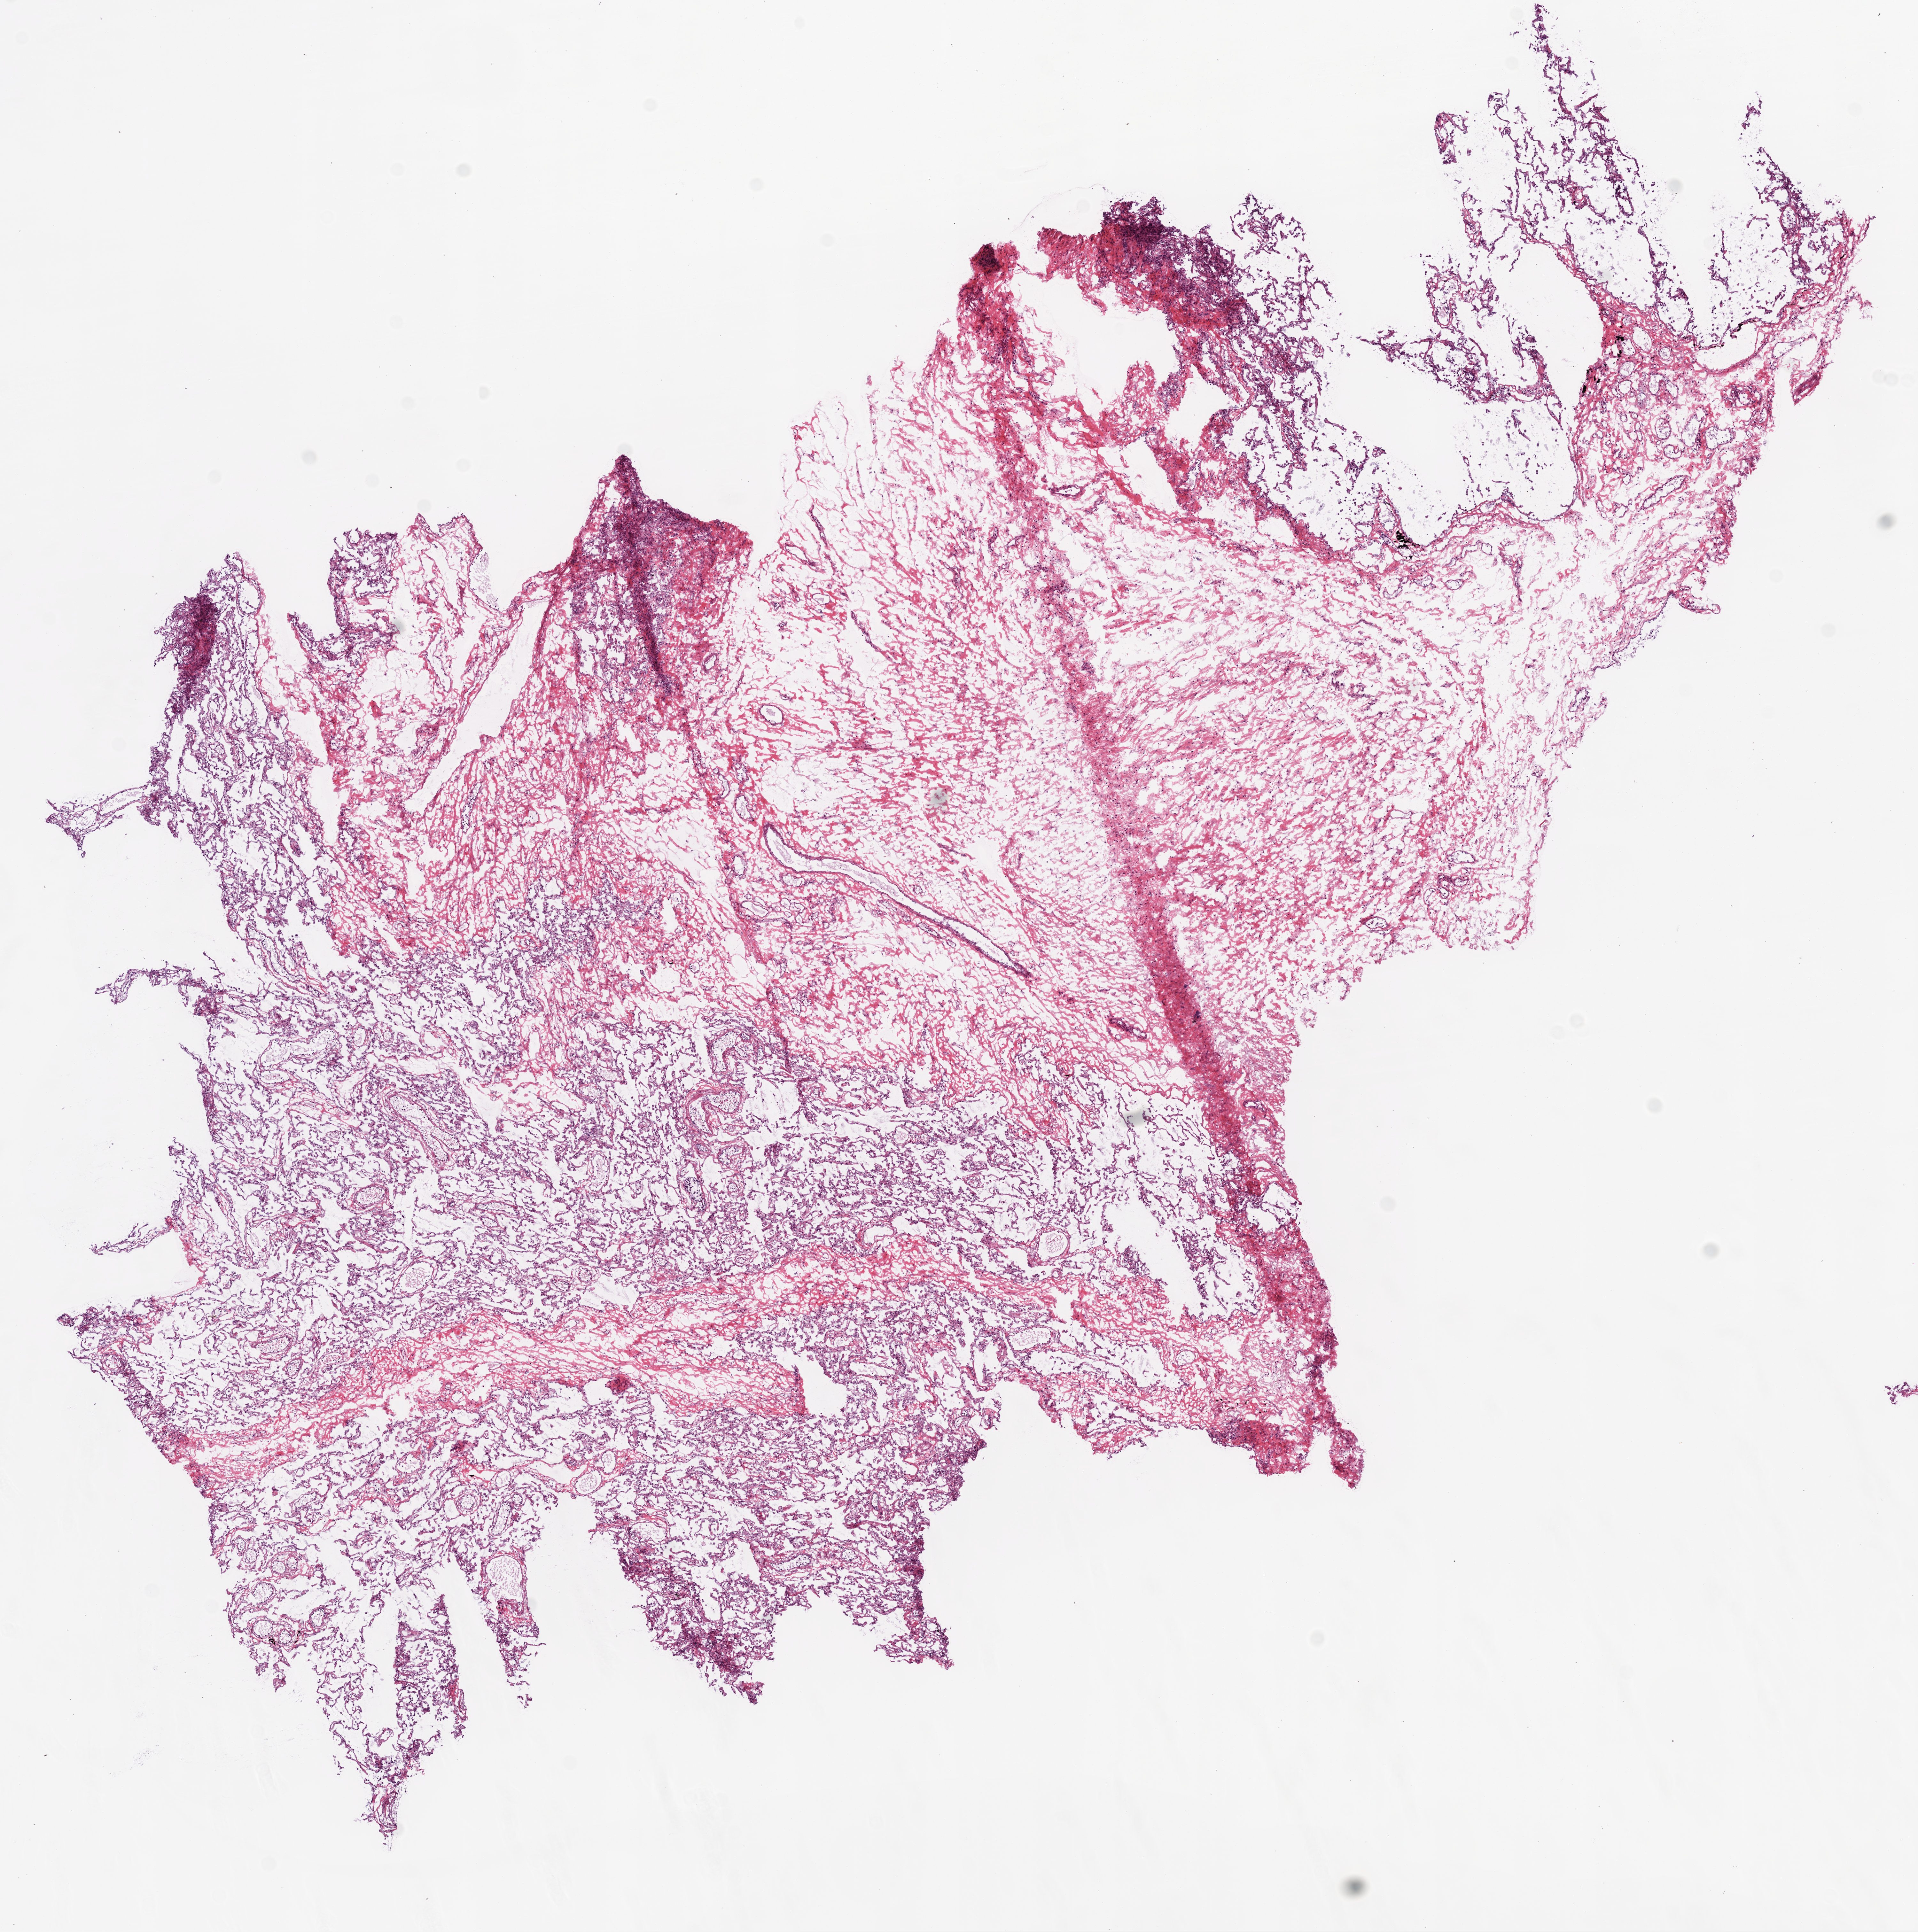
Whole-slide histology image, H&E, whole scanned area (about 12.0 x 12.1 mm) shown as a low-resolution overview. Frozen section. Solid tissue normal (non-tumour tissue) sample from the lung. Male patient; age at initial diagnosis 70 years.
This section: solid tissue normal (non-tumour) sample from the same patient. Patient diagnosis: Squamous cell carcinoma, NOS.